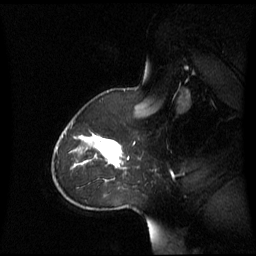
Breast MRI (dynamic contrast-enhanced), one sagittal slice. Slice 46 of 60 in the series (ordered by position). Dynamic contrast-enhanced series, image 2 of 3 at this slice position (ordered by acquisition). 1.5 T. TE 4.2 ms, TR 8.4 ms. 2.8 mm slice thickness. 256 × 256 image matrix, field of view 270 × 270 mm. Female patient, age 43 years. From the clinical record (not read from this slice): setting: breast cancer imaged before/during neoadjuvant chemotherapy; receptor status: triple-negative.
Structures marked on this image (semi-automatically segmented with operator editing):
- analysis volume of interest (the breast-tissue region the enhancement analysis was run in; not a lesion): bounding box <62,124,129,180> (left, top, right, bottom; pixels)
- tumour enhancement mask (voxels above the 70 % enhancement threshold inside the analysis volume of interest): <75,133,124,169>